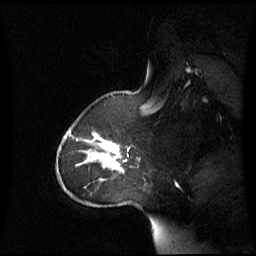
Breast MRI (dynamic contrast-enhanced), one sagittal slice; slice 48 of 60 in the series (ordered by position); dynamic contrast-enhanced series, image 2 of 3 at this slice position (ordered by acquisition); 1.5 T; TE 4.2 ms, TR 8.4 ms; 256 × 256 image matrix, field of view 270 × 270 mm. Patient: female, 43 years. From the clinical record (not read from this slice): setting: breast cancer imaged before/during neoadjuvant chemotherapy; receptor status: triple-negative.
Outlined on this slice (semi-automatically segmented with operator editing):
- analysis volume of interest (the breast-tissue region the enhancement analysis was run in; not a lesion): bounding box <62,124,137,180> (left, top, right, bottom; pixels)
- tumour enhancement mask (voxels above the 70 % enhancement threshold inside the analysis volume of interest): <76,134,121,170>